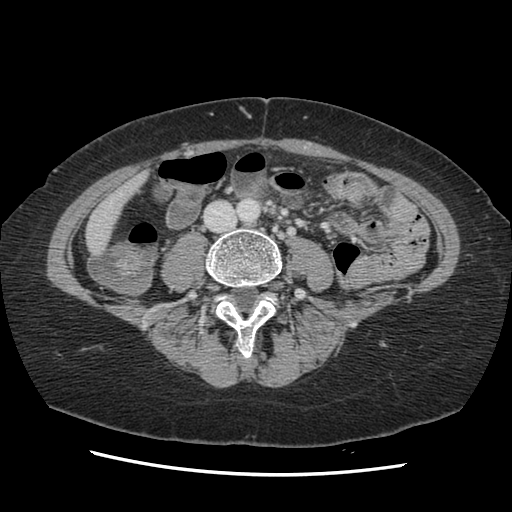
Contrast-enhanced abdominal CT, one axial slice; position 17 of 141 along the scan axis; soft-tissue window (W 400 / L 40 HU); 512 × 512 image matrix, field of view 330 × 330 mm. Female patient, age 61 years. Case-level facts recorded for this patient, not image findings: diagnosis: colorectal cancer liver metastases, imaged before liver resection; multiple liver metastases: no; largest metastasis: 2.4 cm; disease in both lobes: no.
Structures marked on this image (outlined manually by an expert reader):
- liver: box from (x=88, y=174) to (x=145, y=251) px
- planned liver remnant (the part of the liver to remain after resection): (x=88, y=175)–(x=146, y=251)